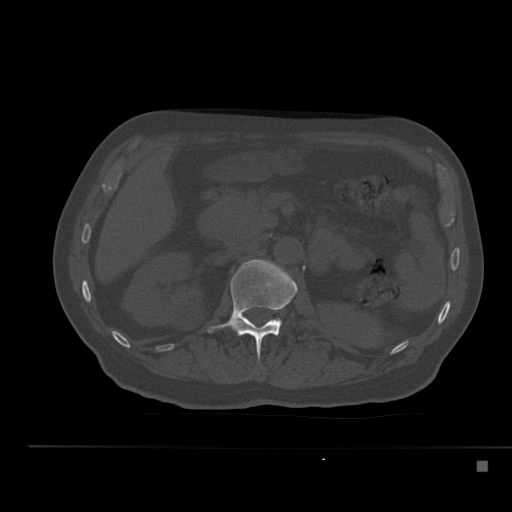
CT including the spine, one axial slice. Position 206 of 517 along the scan axis. Reconstruction kernel Br40s. Bone window (W 1800 / L 400 HU). 1.5 mm slice thickness. 512 × 512 image matrix, field of view 408 × 408 mm. Patient: male, 70 years. Case-level facts recorded for this patient, not image findings: primary cancer: renal.
Annotated regions visible in this slice (semi-automatic segmentation, software-assisted and operator-edited):
- L1 vertebra: box from (x=207, y=259) to (x=298, y=359) px